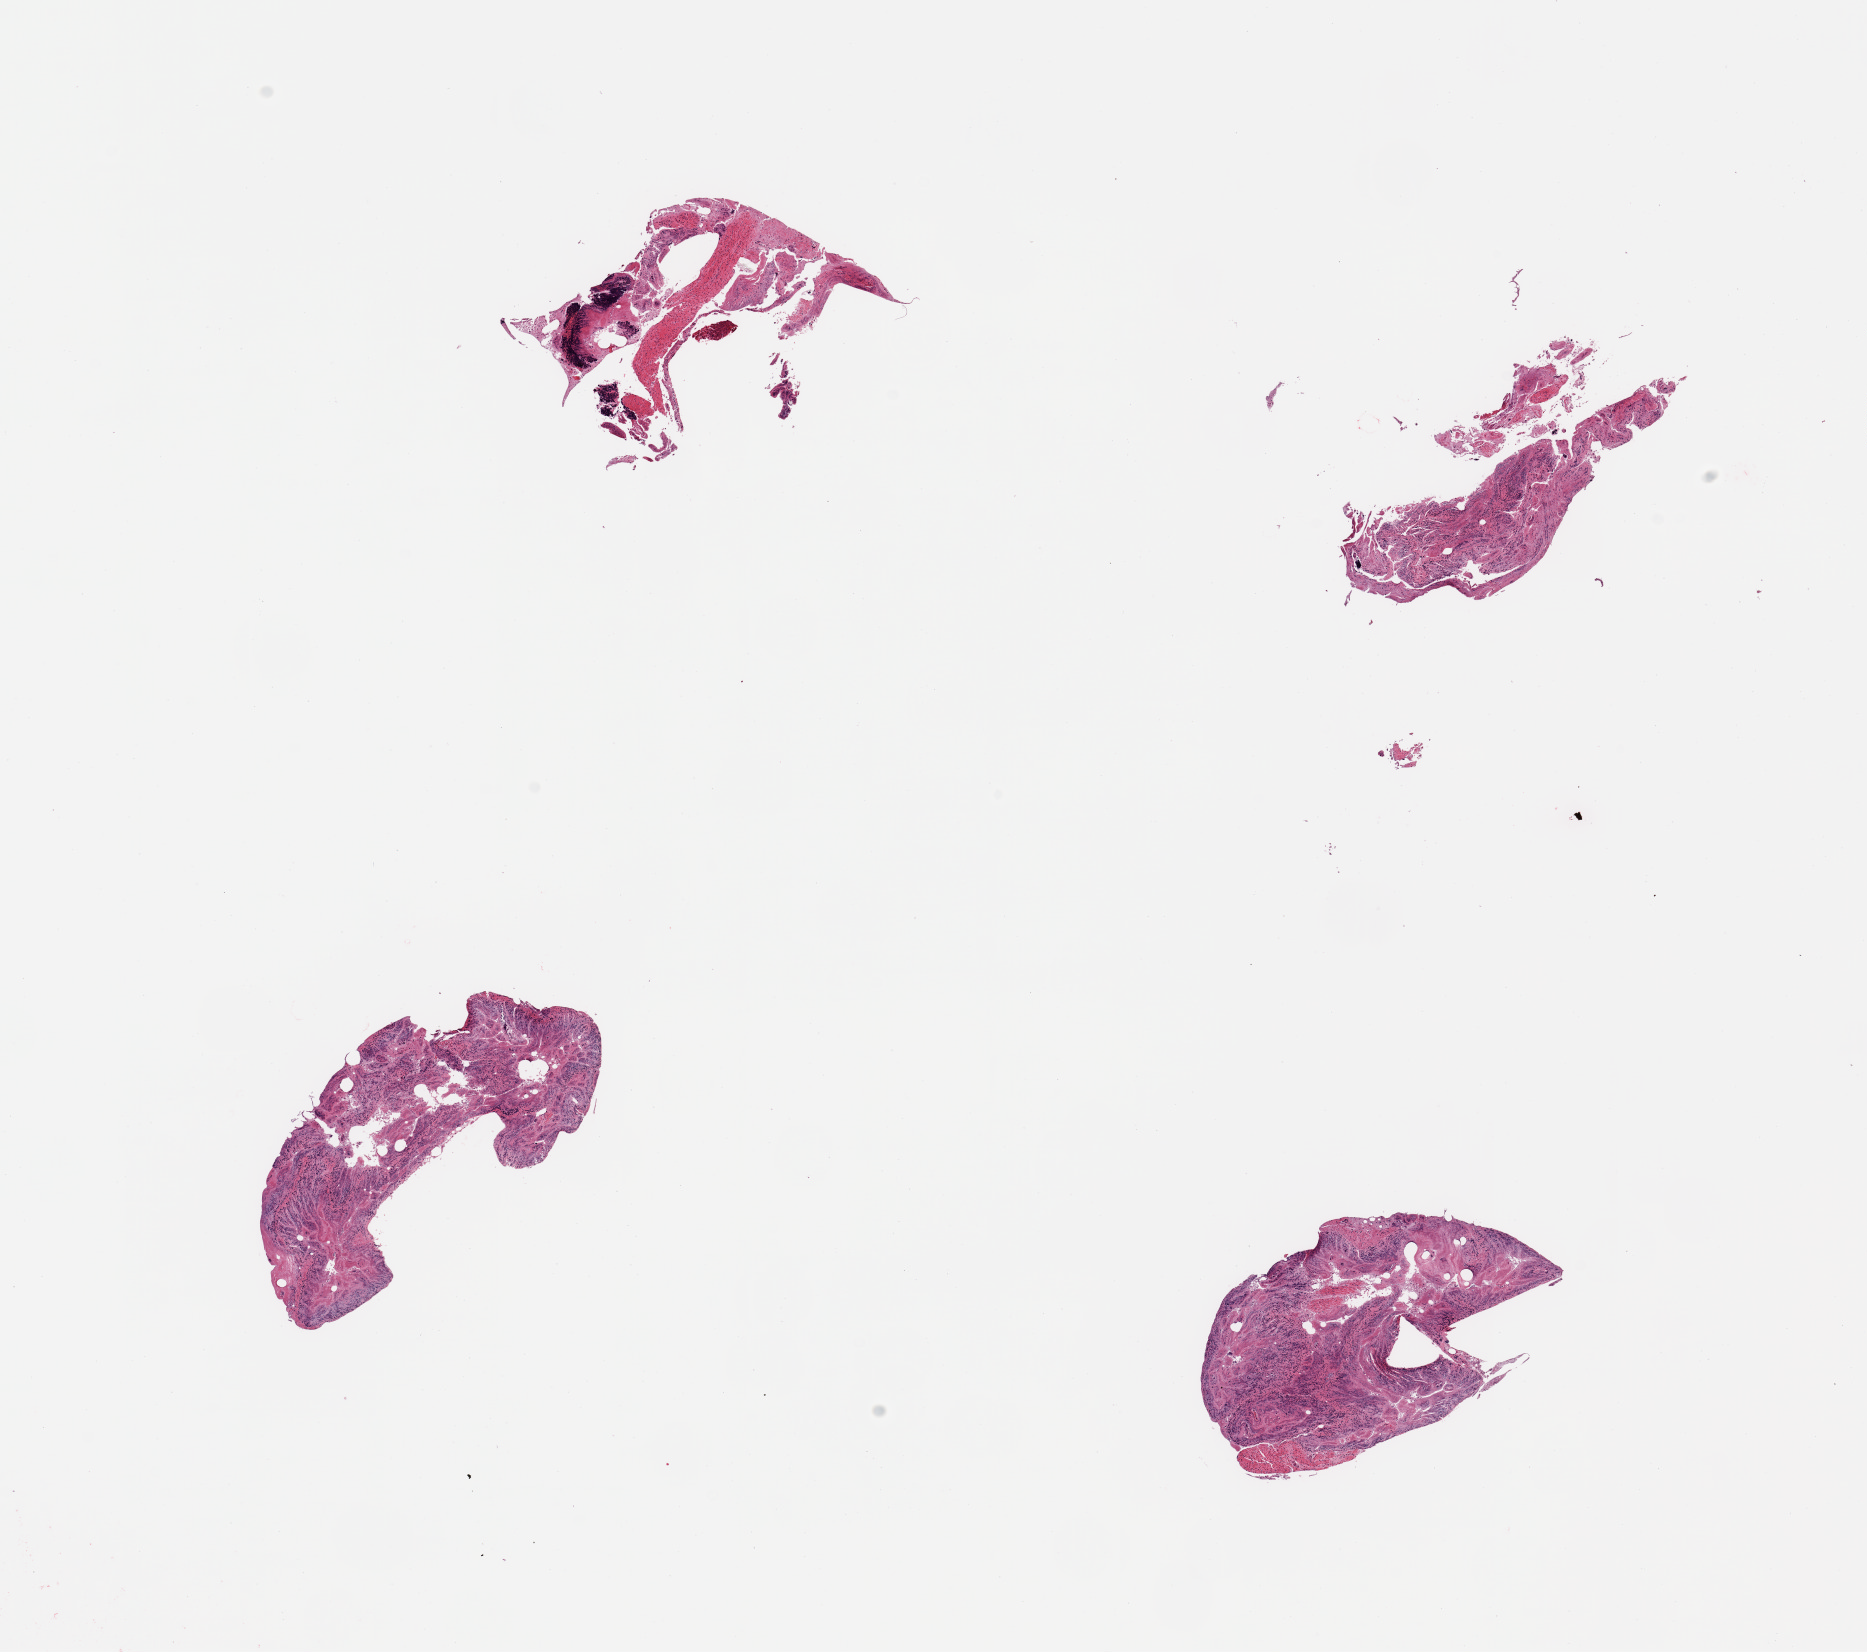
Whole-slide image, H&E stain, whole scanned area (about 14.8 x 13.1 mm, slide scanned at 20x) shown as a low-resolution overview; PAXgene-fixed, paraffin-embedded tissue; sampled site (target tissue): ileum; tissue donor sample. Donor: female.
Review note (as recorded): 4 pieces; totally autolyzed & contains muscle.